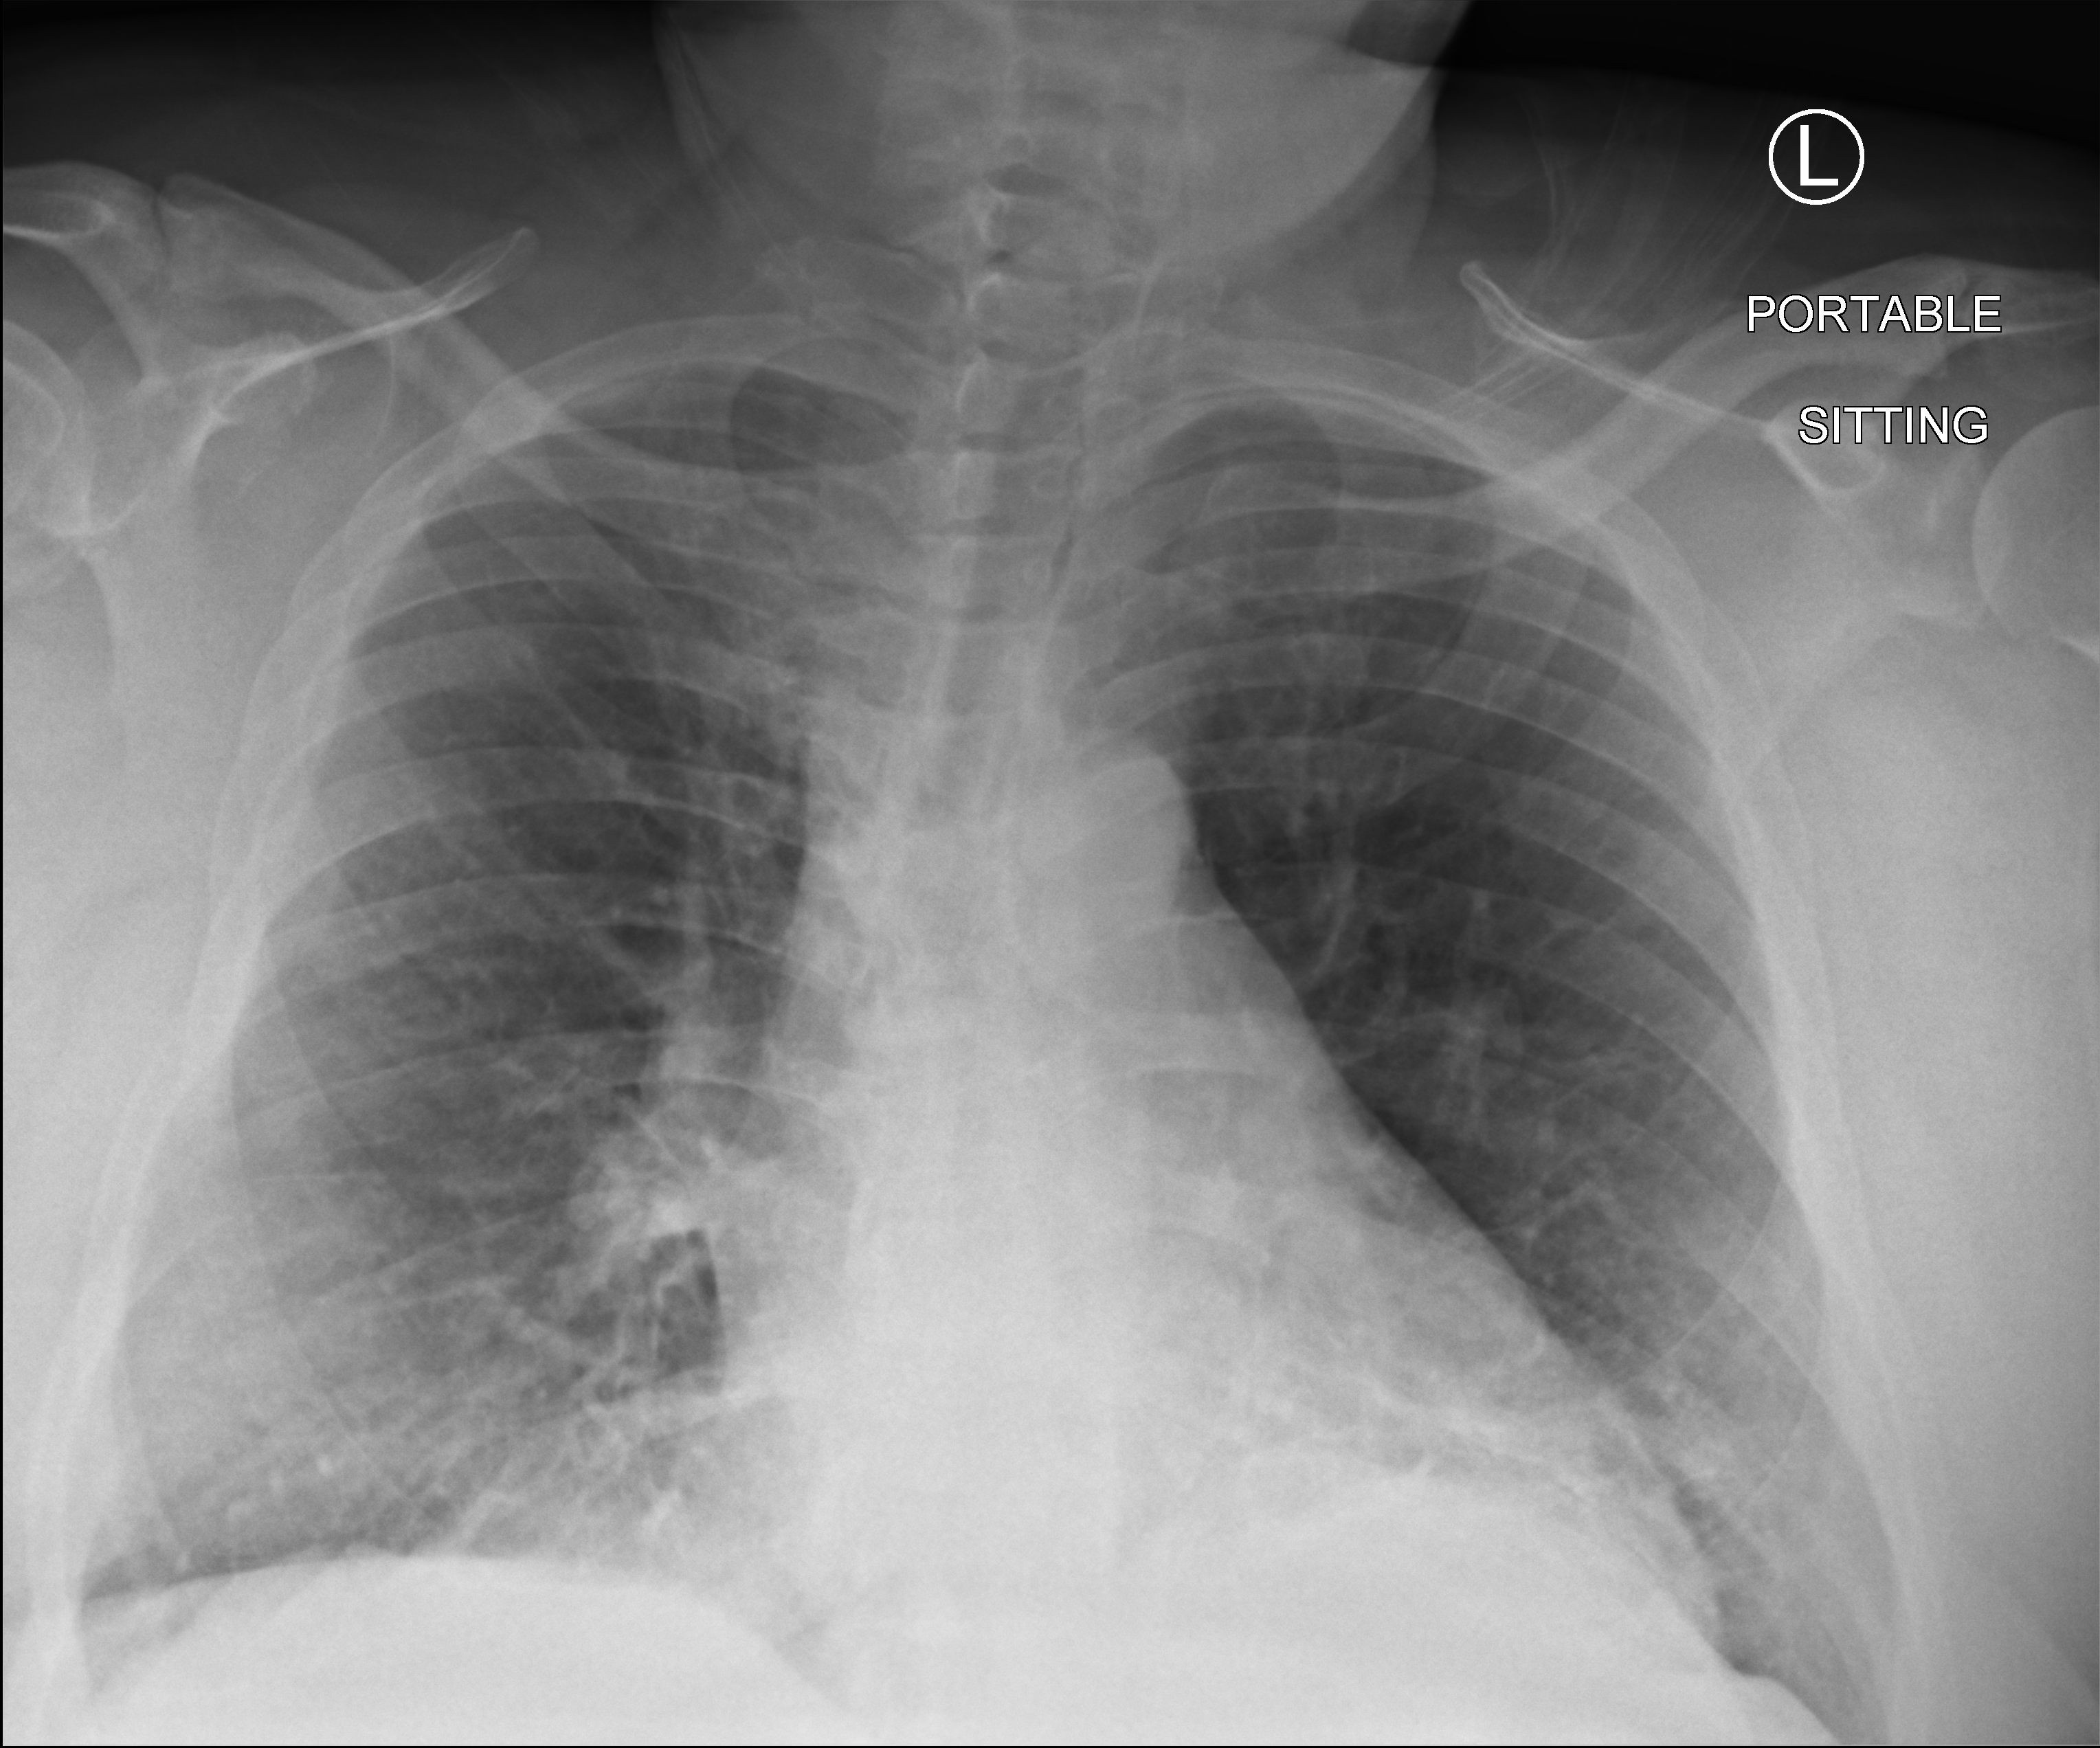
Bedside chest radiograph (computed radiography), anteroposterior (AP) projection. Male patient hospitalised with COVID-19, age 60–74 years.
From the hospital-stay record, not from the radiograph (when in the stay this image was taken is not recorded): length of hospital stay: 34 days.